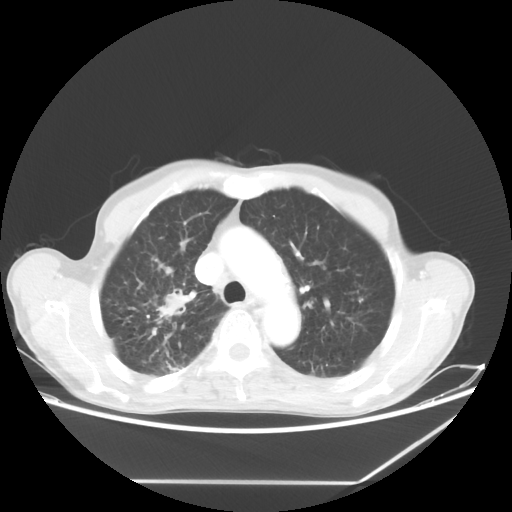
Chest CT, one axial slice. Slice 47 of 65 in the series (ordered by position). Reconstruction kernel STANDARD. 80 kVp. Lung window (W 1500 / L -600 HU). 512 × 512 image matrix. Patient: male, 68 years. From the clinical record (not read from this slice): clinical TNM (as recorded): T3 N3 M0.
Outlined on this slice (bounding box drawn by a radiologist):
- lung tumour (recorded histology: adenocarcinoma): bounding box [x1, y1, x2, y2] px = [145, 283, 206, 335]